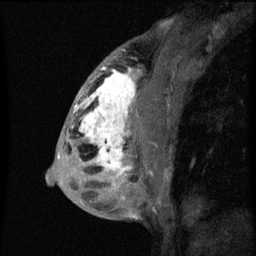
Breast MRI (dynamic contrast-enhanced), one sagittal slice. Slice 32 of 60 in the series (ordered by position). Dynamic contrast-enhanced series, image 2 of 3 at this slice position (ordered by acquisition). 1.5 T. TE 4.2 ms, TR 8 ms. 2 mm slice thickness. 256 × 256 image matrix, field of view 180 × 180 mm. Female patient, age 50 years.
Structures marked on this image (semi-automatic segmentation, software-assisted and operator-edited):
- analysis volume of interest (the breast-tissue region the enhancement analysis was run in; not a lesion): bounding box [x1, y1, x2, y2] px = [66, 64, 141, 187]
- tumour enhancement mask (voxels above the 70 % enhancement threshold inside the analysis volume of interest): [72, 68, 136, 177]